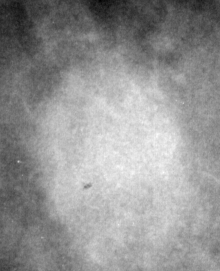
Crop from a digitized film mammogram around one marked abnormality, right breast, MLO view, BI-RADS breast density category 3 (scale 1–4).
Marked abnormality: mass, shape oval, margins ill defined; BI-RADS assessment category 4; subtlety rating 4 on a 1 (subtle) to 5 (obvious) scale; pathology result (as recorded, not read from the image): malignant.